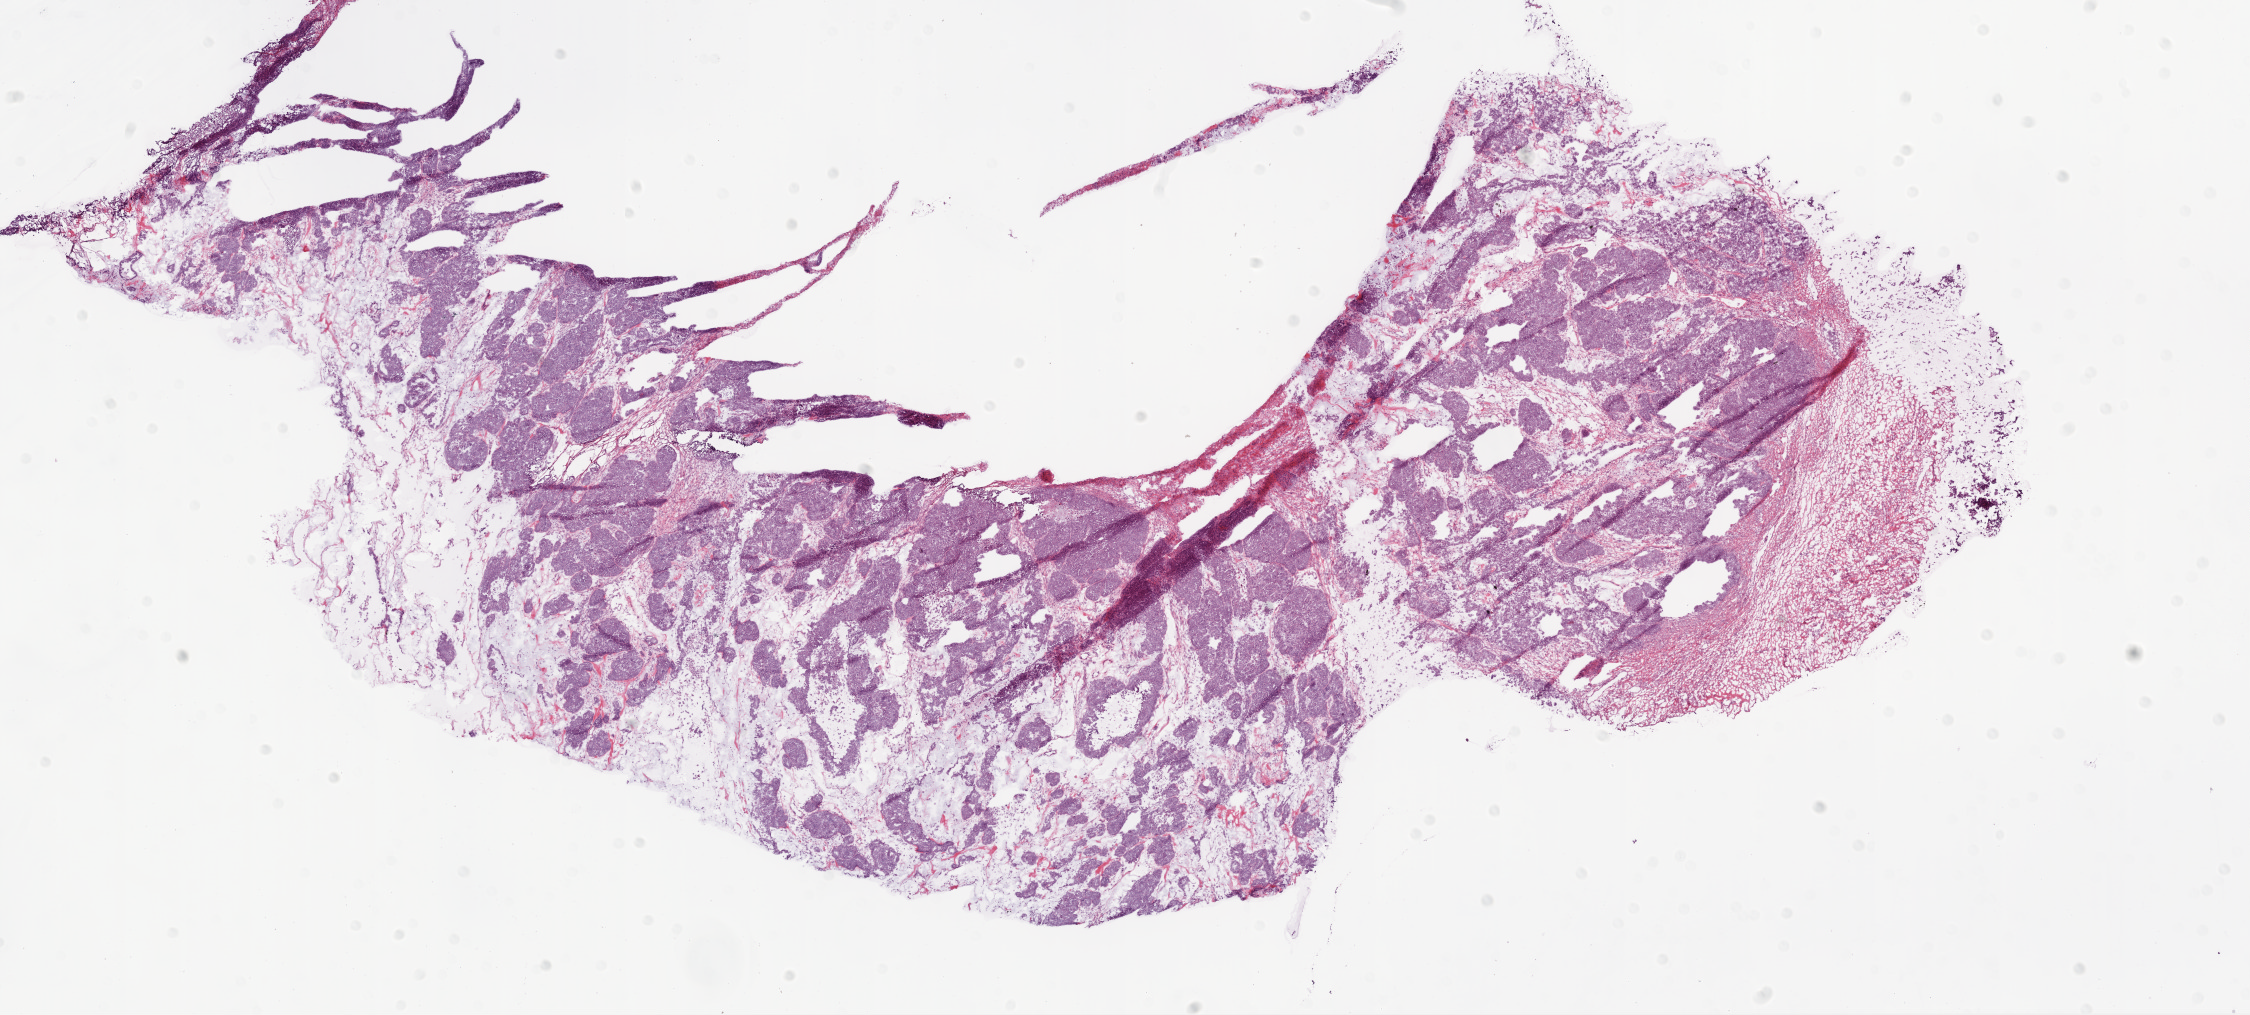
Whole-slide histology image, H&E-stained, shown as a low-resolution overview of the whole scanned area (about 18.1 x 8.1 mm, slide scanned at 20x); frozen section; sample: primary tumour, ovary. Female, age 40 years at initial diagnosis.
Histologic diagnosis: Serous cystadenocarcinoma, NOS.